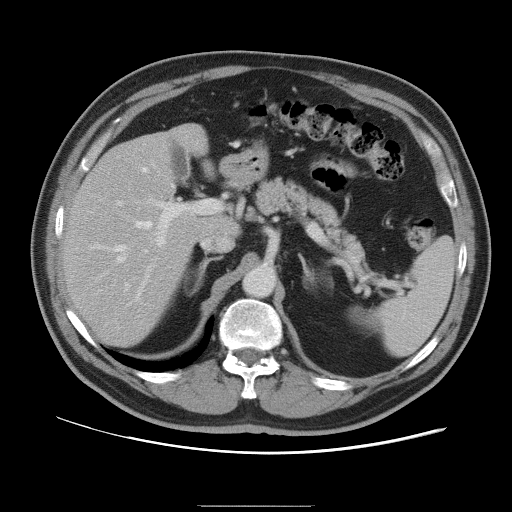
Contrast-enhanced abdominal CT, one axial slice. Slice 61 of 105 in the series (ordered by position). Intravenous contrast given. Soft-tissue window (W 400 / L 40 HU). 512 × 512 image matrix, field of view 399 × 399 mm. Male patient, age 64 years. Case-level facts recorded for this patient, not image findings: diagnosis: colorectal cancer liver metastases, imaged before liver resection; multiple liver metastases: yes.
Structures marked on this image (expert manual segmentation):
- hepatic veins: bounding box [x1, y1, x2, y2] px = [115, 168, 152, 286]
- liver: [64, 125, 235, 346]
- planned liver remnant (the part of the liver to remain after resection): [64, 135, 236, 346]
- portal vein (with intrahepatic branches): [117, 199, 193, 318]